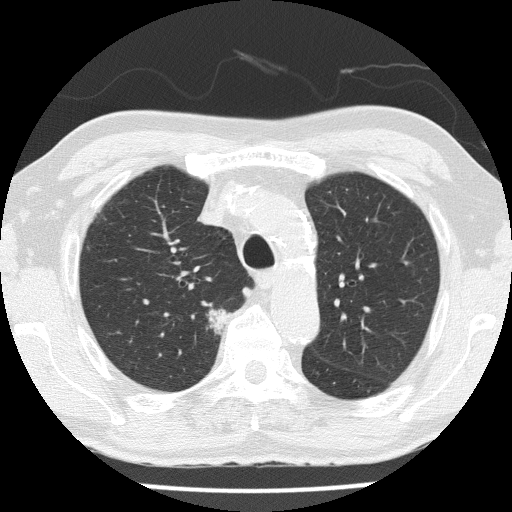
Low-dose screening chest CT, one axial slice; position 110 of 153 along the scan axis; reconstruction kernel FC51; lung window (W 1500 / L -600 HU); 512 × 512 image matrix, field of view 323 × 323 mm.
Outlined on this slice (manually delineated by an expert):
- lesion 1 (tumor, upper lobe of right lung): bounding box [x1, y1, x2, y2] px = [209, 309, 228, 333]